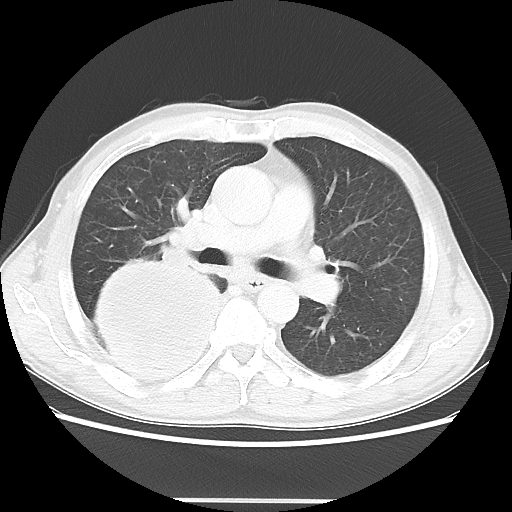
Chest CT, one axial slice. Slice 29 of 48 in the series (ordered by position). Reconstruction kernel LUNG. 100 kVp. Lung window (W 1500 / L -600 HU). 512 × 512 image matrix, field of view 361 × 361 mm. Patient: male, 66 years. From the clinical record (not read from this slice): clinical TNM (as recorded): T4 N1 M1.
Annotated regions visible in this slice (bounding box drawn by a radiologist):
- lung tumour (recorded histology: small cell carcinoma): bounding box <92,251,231,398> (left, top, right, bottom; pixels)